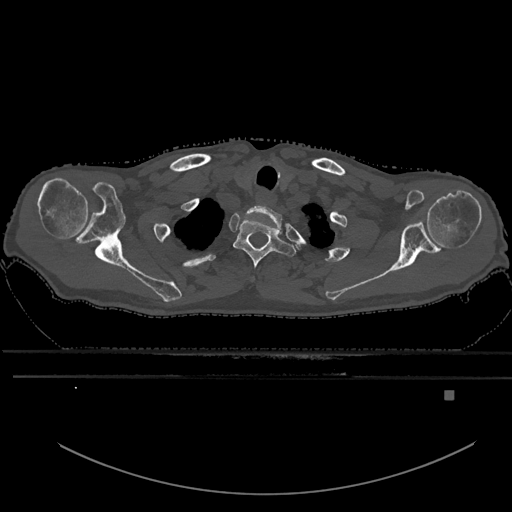
CT including the spine, one axial slice. Bone window (W 1800 / L 400 HU). 0.5 mm slice thickness. 512 × 512 image matrix. Patient: male, 82 years. From the clinical record (not read from this slice): primary cancer: prostate.
Structures marked on this image (semi-automatically segmented with operator editing):
- T1 vertebra: bounding box [x1, y1, x2, y2] px = [233, 219, 296, 269]